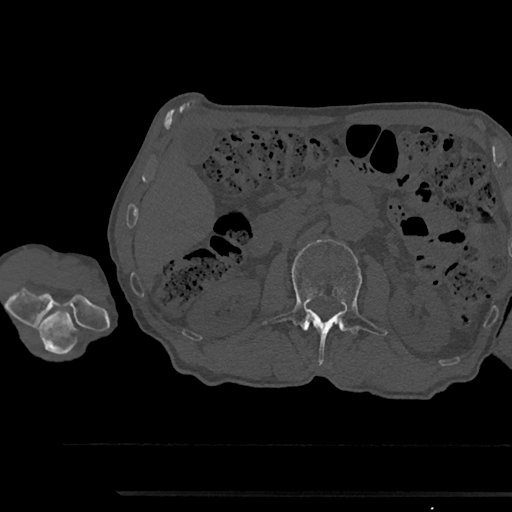
CT including the spine, one axial slice; slice 571 of 797 in the series (ordered by position); reconstruction kernel Br40s/3; bone window (W 1800 / L 400 HU); 0.5 mm slice thickness; 512 × 512 image matrix, field of view 367 × 367 mm. Male patient, age 79 years. From the clinical record (not read from this slice): primary cancer: prostate.
Outlined on this slice (semi-automatic segmentation, software-assisted and operator-edited):
- L2 vertebra: bounding box (x1, y1, x2, y2) in pixels: (262, 240, 387, 364)